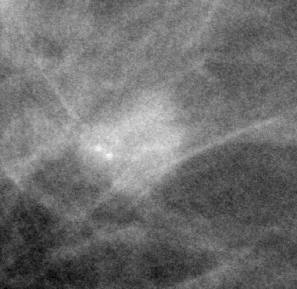
Cropped region of a digitized screen-film mammogram centred on a radiologist-marked abnormality, right breast, MLO view, BI-RADS breast density category 1 (scale 1–4).
- Finding: calcifications, morphology punctate, distribution clustered; BI-RADS assessment category 4; pathology result (as recorded, not read from the image): benign.